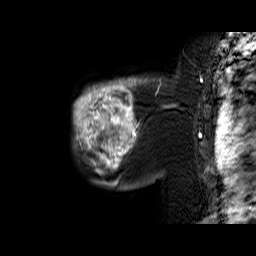
Breast MRI (dynamic contrast-enhanced), one sagittal slice; position 51 of 60 along the scan axis; dynamic contrast-enhanced series, time point 2 of 6 at this slice position (early post-contrast); 1.5 T; TE 6.4 ms, TR 32.9 ms; 256 × 256 image matrix. Female patient. Case-level facts recorded for this patient, not image findings: setting: breast cancer imaged before/during neoadjuvant chemotherapy; receptor status: triple-negative.
Outlined on this slice (semi-automatic segmentation, software-assisted and operator-edited):
- analysis volume of interest (the breast-tissue region the enhancement analysis was run in; not a lesion): bounding box (x1, y1, x2, y2) in pixels: (74, 78, 159, 174)
- tumour enhancement mask (voxels above the 100 % enhancement threshold inside the analysis volume of interest): (74, 78, 159, 173)